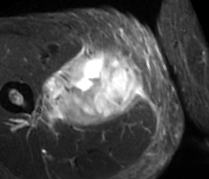
MRI of an extremity soft-tissue mass, one axial slice; STIR; MR volume resampled by the dataset authors to the PET/CT grid (not the native acquisition matrix); 3.27 mm slice thickness; 209 × 179 image matrix, field of view 204 × 175 mm. Male patient. Case-level facts recorded for this patient, not image findings: histological type: undifferentiated - pleiomorphic; grade: high; site of the primary tumour: right thigh.
Outlined on this slice (expert contour drawn on MRI and transferred to this co-registered scan by the dataset authors):
- gross tumour volume including surrounding oedema: bounding box (x1, y1, x2, y2) in pixels: (32, 44, 143, 125)
- gross tumour volume (mass): (60, 50, 141, 125)